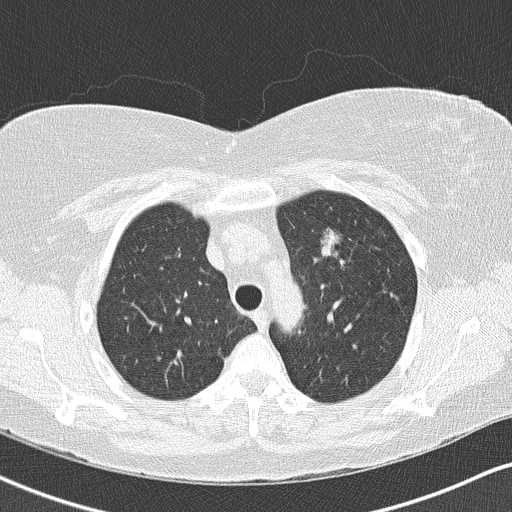
Axial slice from a low-dose chest CT screening exam, second screening round (one year after baseline), lung window (W 1500 / L -600 HU), lung (sharp) reconstruction kernel (B50f), slice 114 of 146 in the series. Female participant, aged 57 years at enrolment.
- Expert-annotated lung lesion, bounding box <312,221,350,264> (left, top, right, bottom; pixels).
- The screening reader recorded 3 non-calcified nodules or masses ≥4 mm on this exam (left upper lobe, right upper lobe, right middle lobe); which of them this box marks is not recorded.
- Official screen result: positive, other.
- Later outcome: lung cancer diagnosed 75 days after this screen — adenocarcinoma, NOS, left upper lobe, poorly differentiated (G3), stage IA (AJCC 6th edition), 24 mm at pathology.